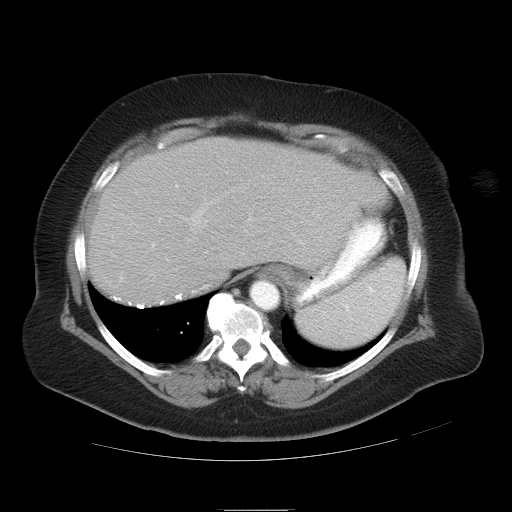
Contrast-enhanced abdominal CT, one axial slice; position 29 of 37 along the scan axis; reconstruction kernel STANDARD; soft-tissue window (W 400 / L 40 HU); 512 × 512 image matrix, field of view 422 × 422 mm. Female patient, age 68 years. Case-level facts recorded for this patient, not image findings: diagnosis: colorectal cancer liver metastases, imaged before liver resection; multiple liver metastases: no; largest metastasis: 2 cm; disease in both lobes: no.
Structures marked on this image (outlined manually by an expert reader):
- hepatic veins: box from (x=174, y=175) to (x=274, y=245) px
- liver: (x=88, y=138)–(x=391, y=308)
- planned liver remnant (the part of the liver to remain after resection): (x=90, y=138)–(x=391, y=307)
- portal vein (with intrahepatic branches): (x=151, y=185)–(x=178, y=248)